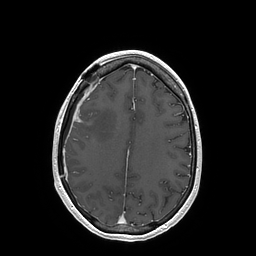
Brain MRI from a brain-tumour surgery series, one axial slice; position 60 of 202 along the scan axis; T1-weighted post-contrast; 256 × 256 image matrix. From the clinical record (not read from this slice): histopathology: Glioblastoma; WHO grade: 4; IDH mutation: no; tumour location: Right Insular.
Annotated regions visible in this slice (manually delineated by an expert):
- tumour: box from (x=76, y=119) to (x=81, y=122) px